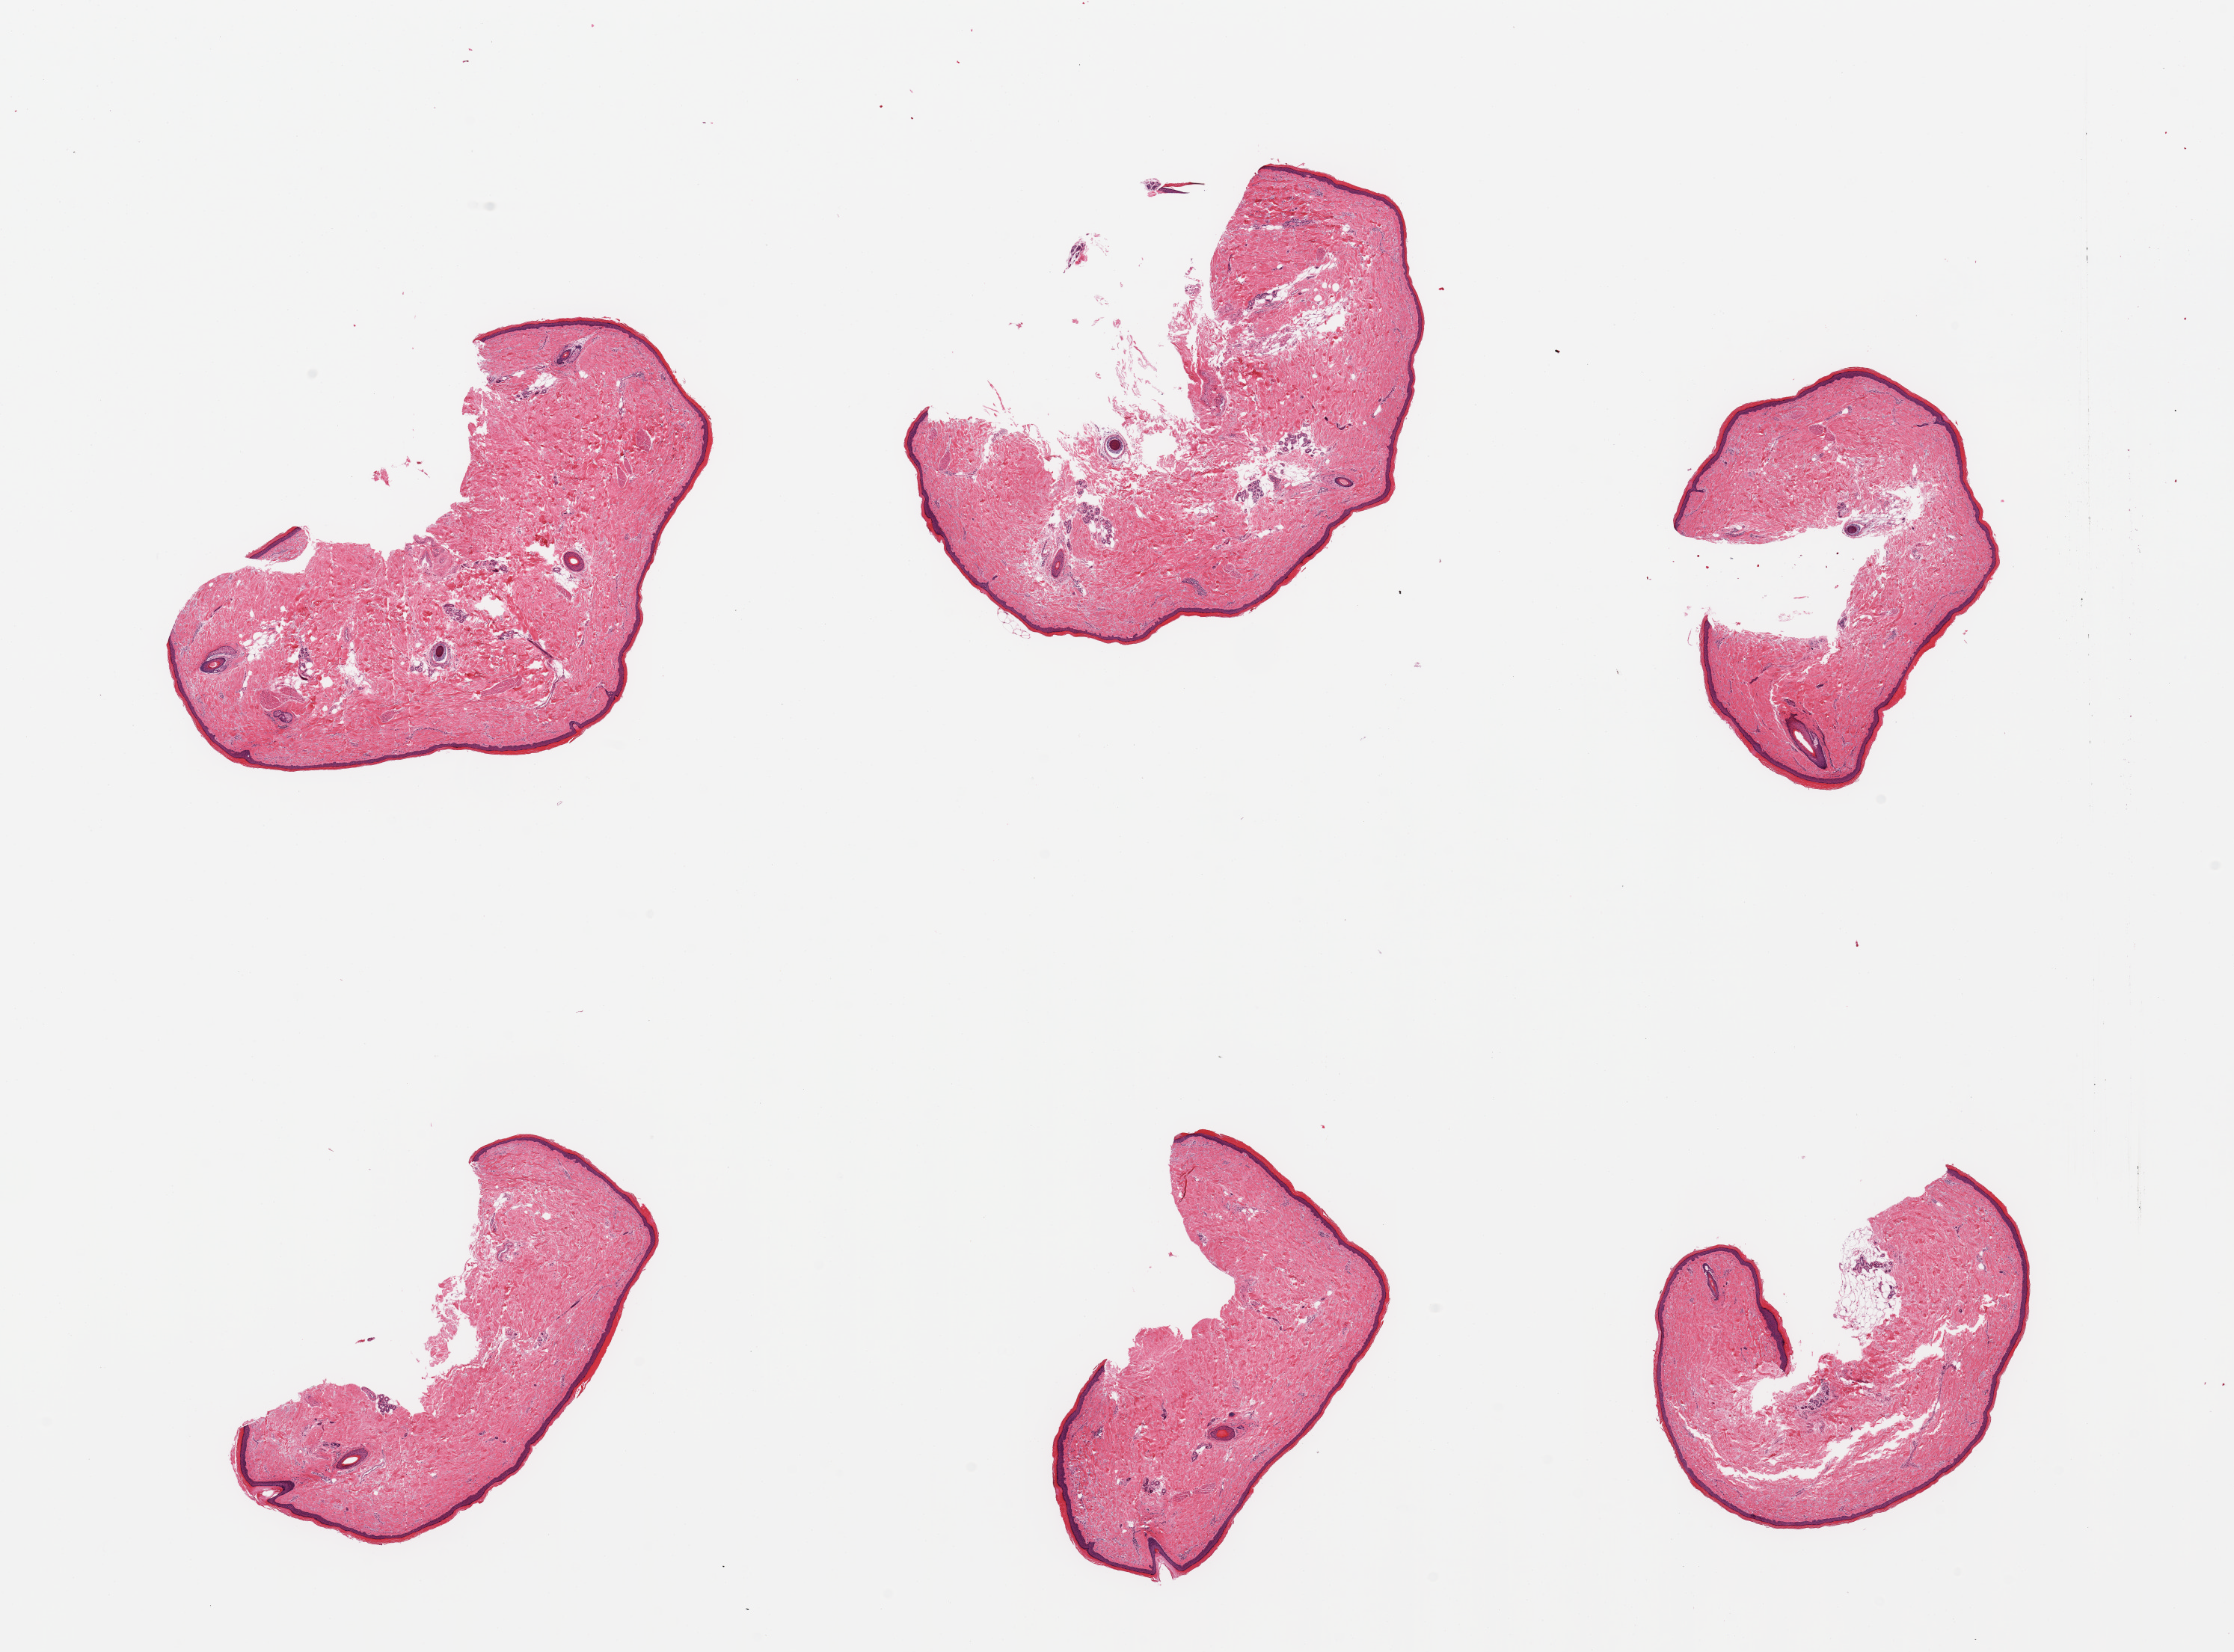
Haematoxylin and eosin whole-slide image, whole scanned area (about 23.6 x 17.5 mm, acquisition: 20x scan) shown as a low-resolution overview, PAXgene-fixed, paraffin-embedded tissue, sampled site (target tissue): skin of lower leg, donor tissue sample. Donor sex: female.
* review note (as recorded): 6 pieces, trace dermal fat; squamous epithelium is ~40 microns